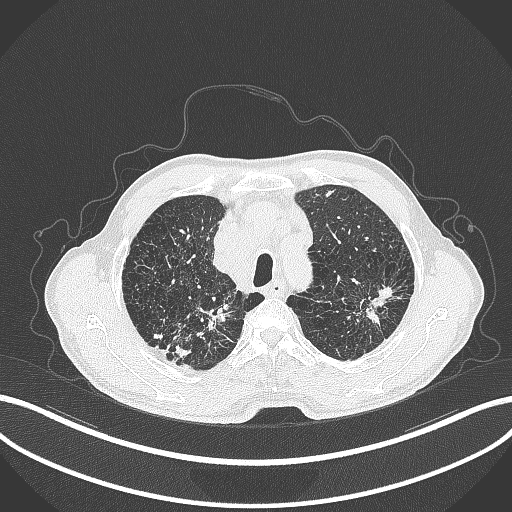
Chest CT, one axial slice. Position 362 of 463 along the scan axis. Reconstruction kernel B70f. 120 kVp. Lung window (W 1500 / L -600 HU). 1 mm slice thickness. 512 × 512 image matrix. Patient: male, 74 years. Case-level facts recorded for this patient, not image findings: clinical TNM (as recorded): T2a N1 M0.
Outlined on this slice (bounding box drawn by a radiologist):
- lung tumour (recorded histology: adenocarcinoma): bounding box (x1, y1, x2, y2) in pixels: (362, 282, 396, 326)